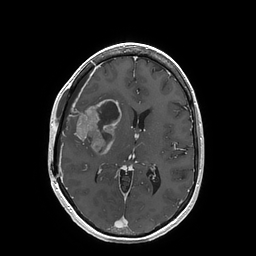
Brain MRI from a brain-tumour surgery series, one axial slice; slice 81 of 202 in the series (ordered by position); T1-weighted post-contrast; 256 × 256 image matrix, field of view 250 × 250 mm. From the clinical record (not read from this slice): histopathology: Glioblastoma; WHO grade: 4; IDH mutation: no; tumour location: Right Insular.
Outlined on this slice (outlined manually by an expert reader):
- tumour: bounding box [x1, y1, x2, y2] px = [69, 99, 122, 155]